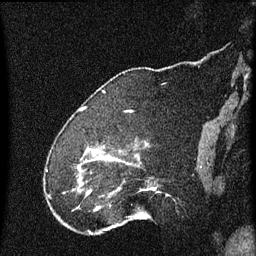
Breast MRI (dynamic contrast-enhanced), one sagittal slice. Position 16 of 60 along the scan axis. Dynamic contrast-enhanced series, image 2 of 4 at this slice position (ordered by acquisition). 1.5 T. TE 4.2 ms, TR 8 ms. 2 mm slice thickness. 256 × 256 image matrix, field of view 180 × 180 mm. Patient: female, 52 years.
Outlined on this slice (semi-automatically segmented with operator editing):
- analysis volume of interest (the breast-tissue region the enhancement analysis was run in; not a lesion): bounding box [x1, y1, x2, y2] px = [73, 148, 166, 219]
- tumour enhancement mask (voxels above the 70 % enhancement threshold inside the analysis volume of interest): [87, 160, 112, 193]